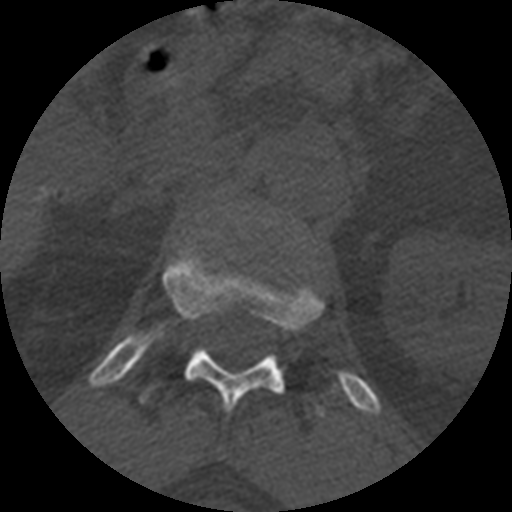
CT including the spine, one axial slice. Slice 382 of 399 in the series (ordered by position). Bone window (W 1800 / L 400 HU). 1.25 mm slice thickness. 512 × 512 image matrix, field of view 160 × 160 mm. Patient age 71 years. From the clinical record (not read from this slice): primary cancer: prostate.
Structures marked on this image (semi-automatically segmented with operator editing):
- T12 vertebra: bounding box (x1, y1, x2, y2) in pixels: (142, 242, 323, 414)